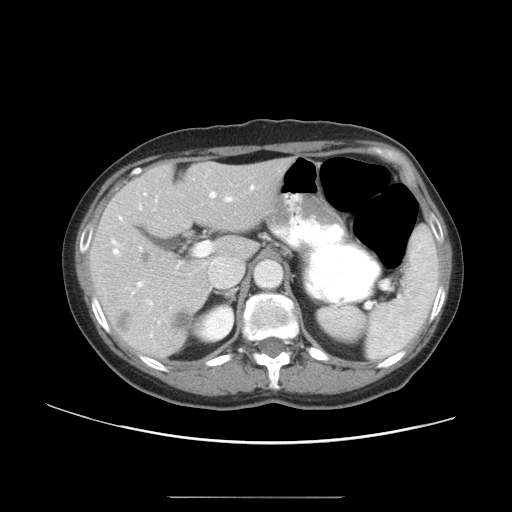
Contrast-enhanced abdominal CT, one axial slice; slice 30 of 50 in the series (ordered by position); reconstruction kernel STANDARD; intravenous contrast given; soft-tissue window (W 400 / L 40 HU); 512 × 512 image matrix, field of view 389 × 389 mm. Female patient, age 58 years. Case-level facts recorded for this patient, not image findings: diagnosis: colorectal cancer liver metastases, imaged before liver resection; multiple liver metastases: yes; largest metastasis: 7.3 cm.
Outlined on this slice (outlined manually by an expert reader):
- hepatic veins: bounding box (x1, y1, x2, y2) in pixels: (114, 185, 254, 254)
- liver: (92, 161, 286, 359)
- planned liver remnant (the part of the liver to remain after resection): (180, 161, 286, 257)
- portal vein (with intrahepatic branches): (112, 192, 216, 287)
- liver metastasis: (176, 315, 191, 331)
- liver metastasis: (120, 315, 130, 328)
- liver metastasis: (143, 254, 151, 264)
- liver metastasis: (122, 254, 152, 328)
- liver metastasis: (141, 251, 151, 264)